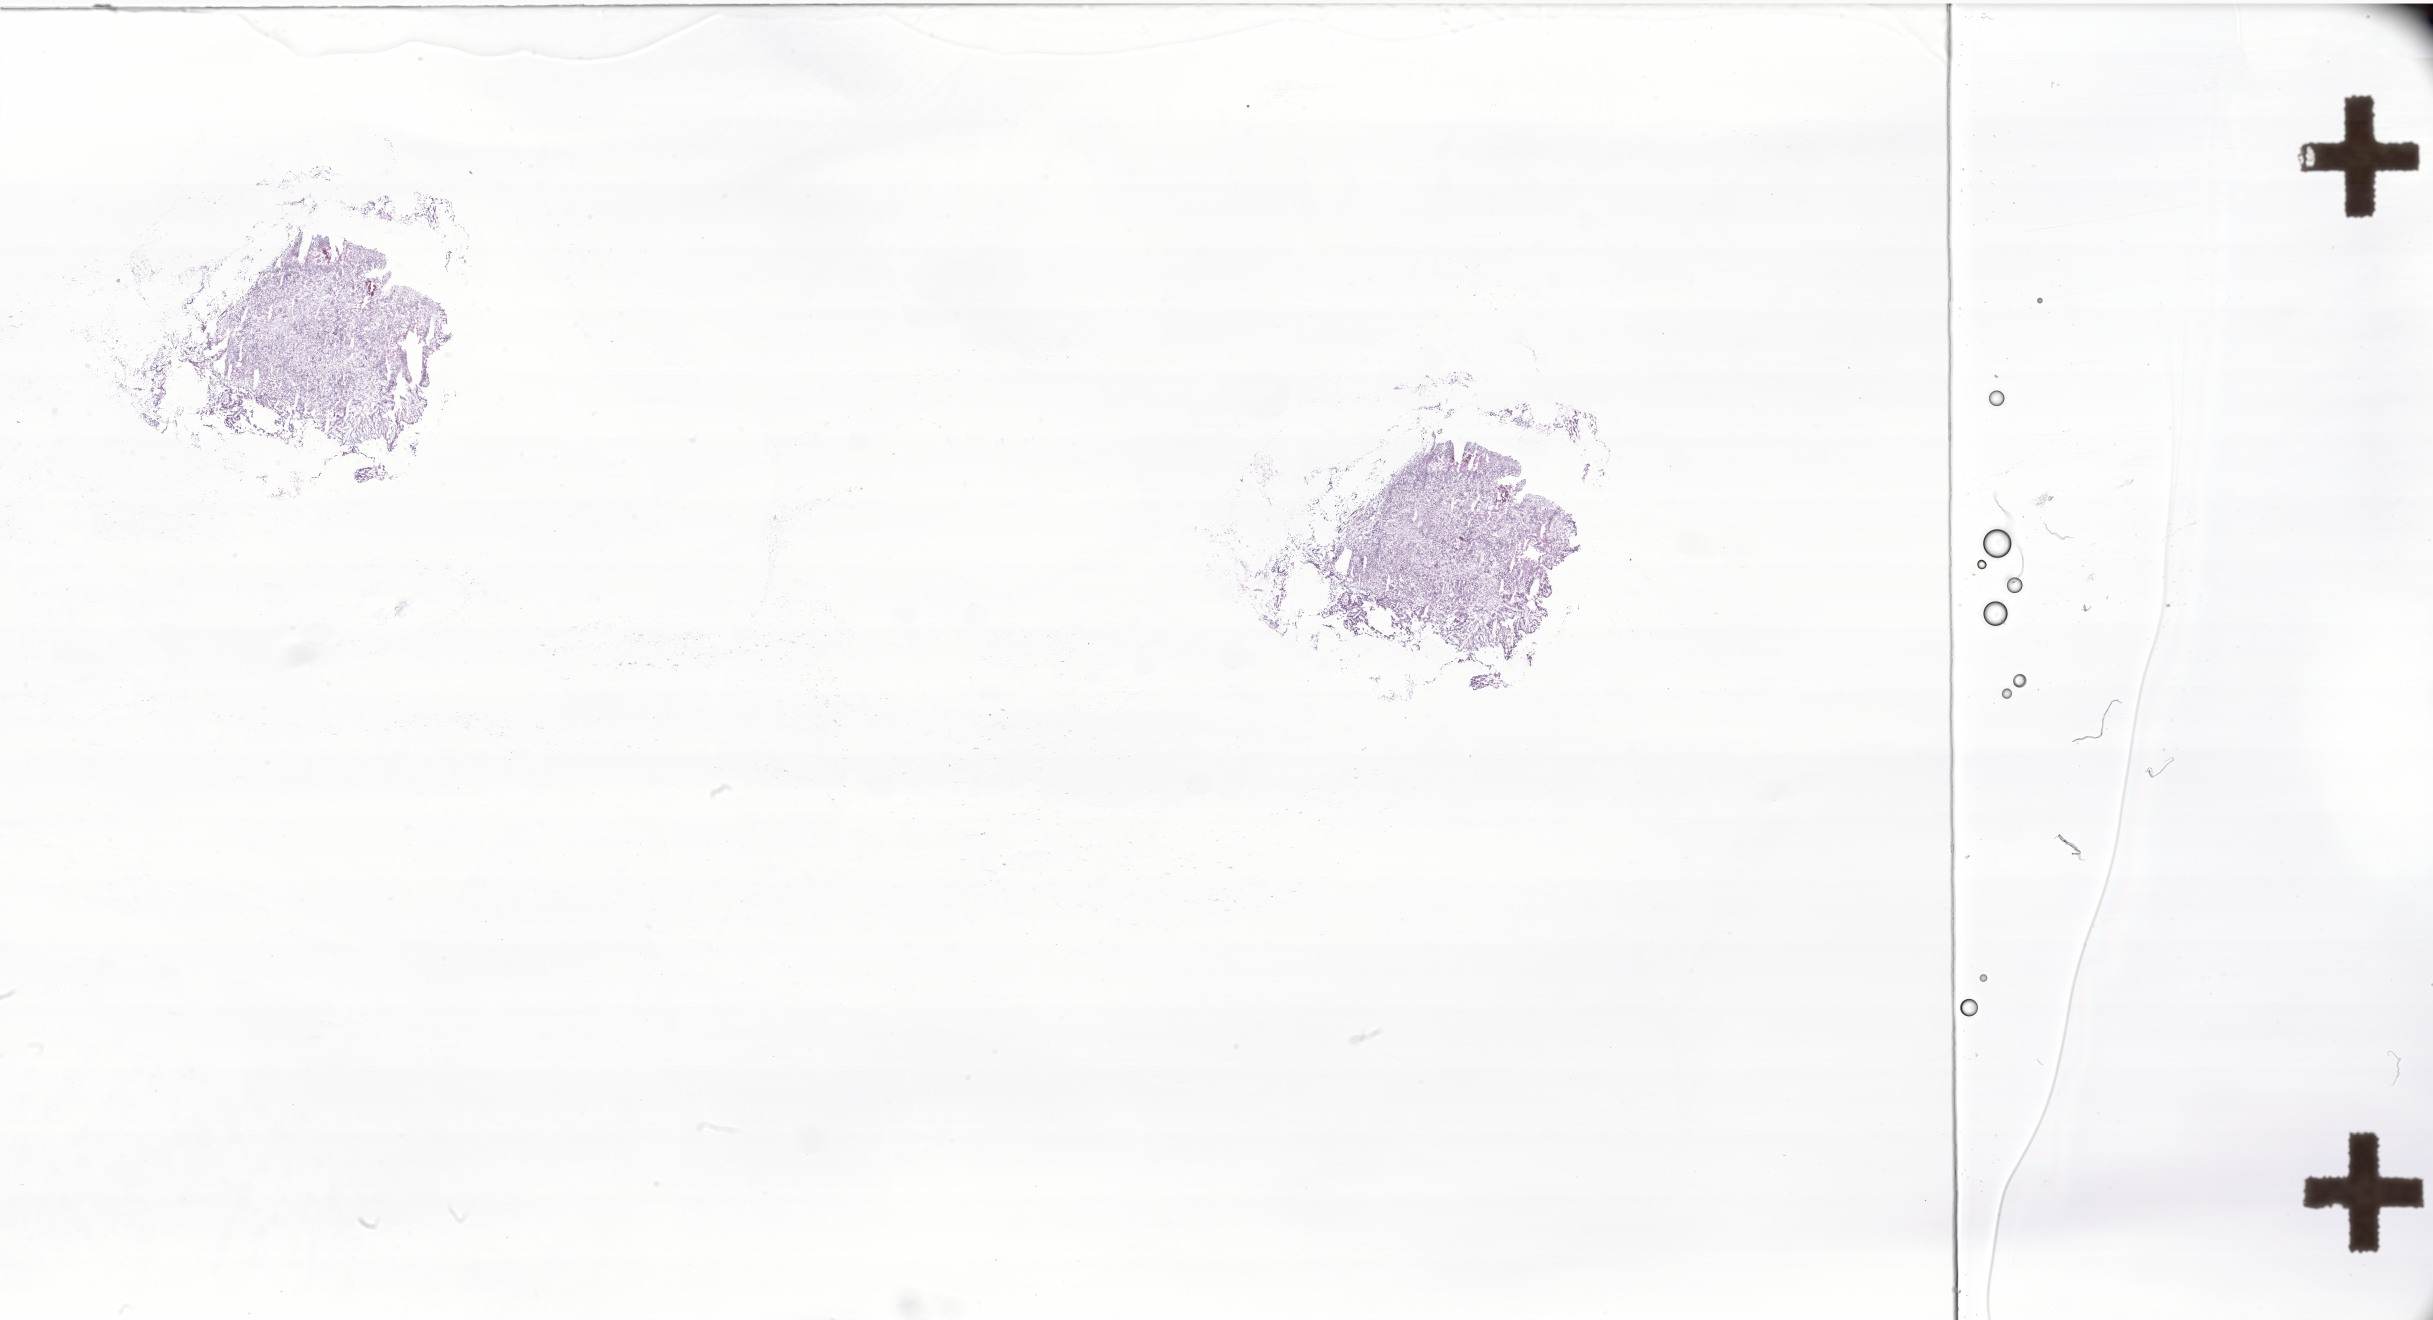
Digitized hematoxylin and eosin (H&E)-stained section of tumor tissue from the adrenal gland — low-resolution overview of the scanned area, about 41.0 x 22.3 mm, frozen section (OCT-embedded). Patient: male, age 180 days.
* recorded diagnosis: Neuroblastoma, NOS